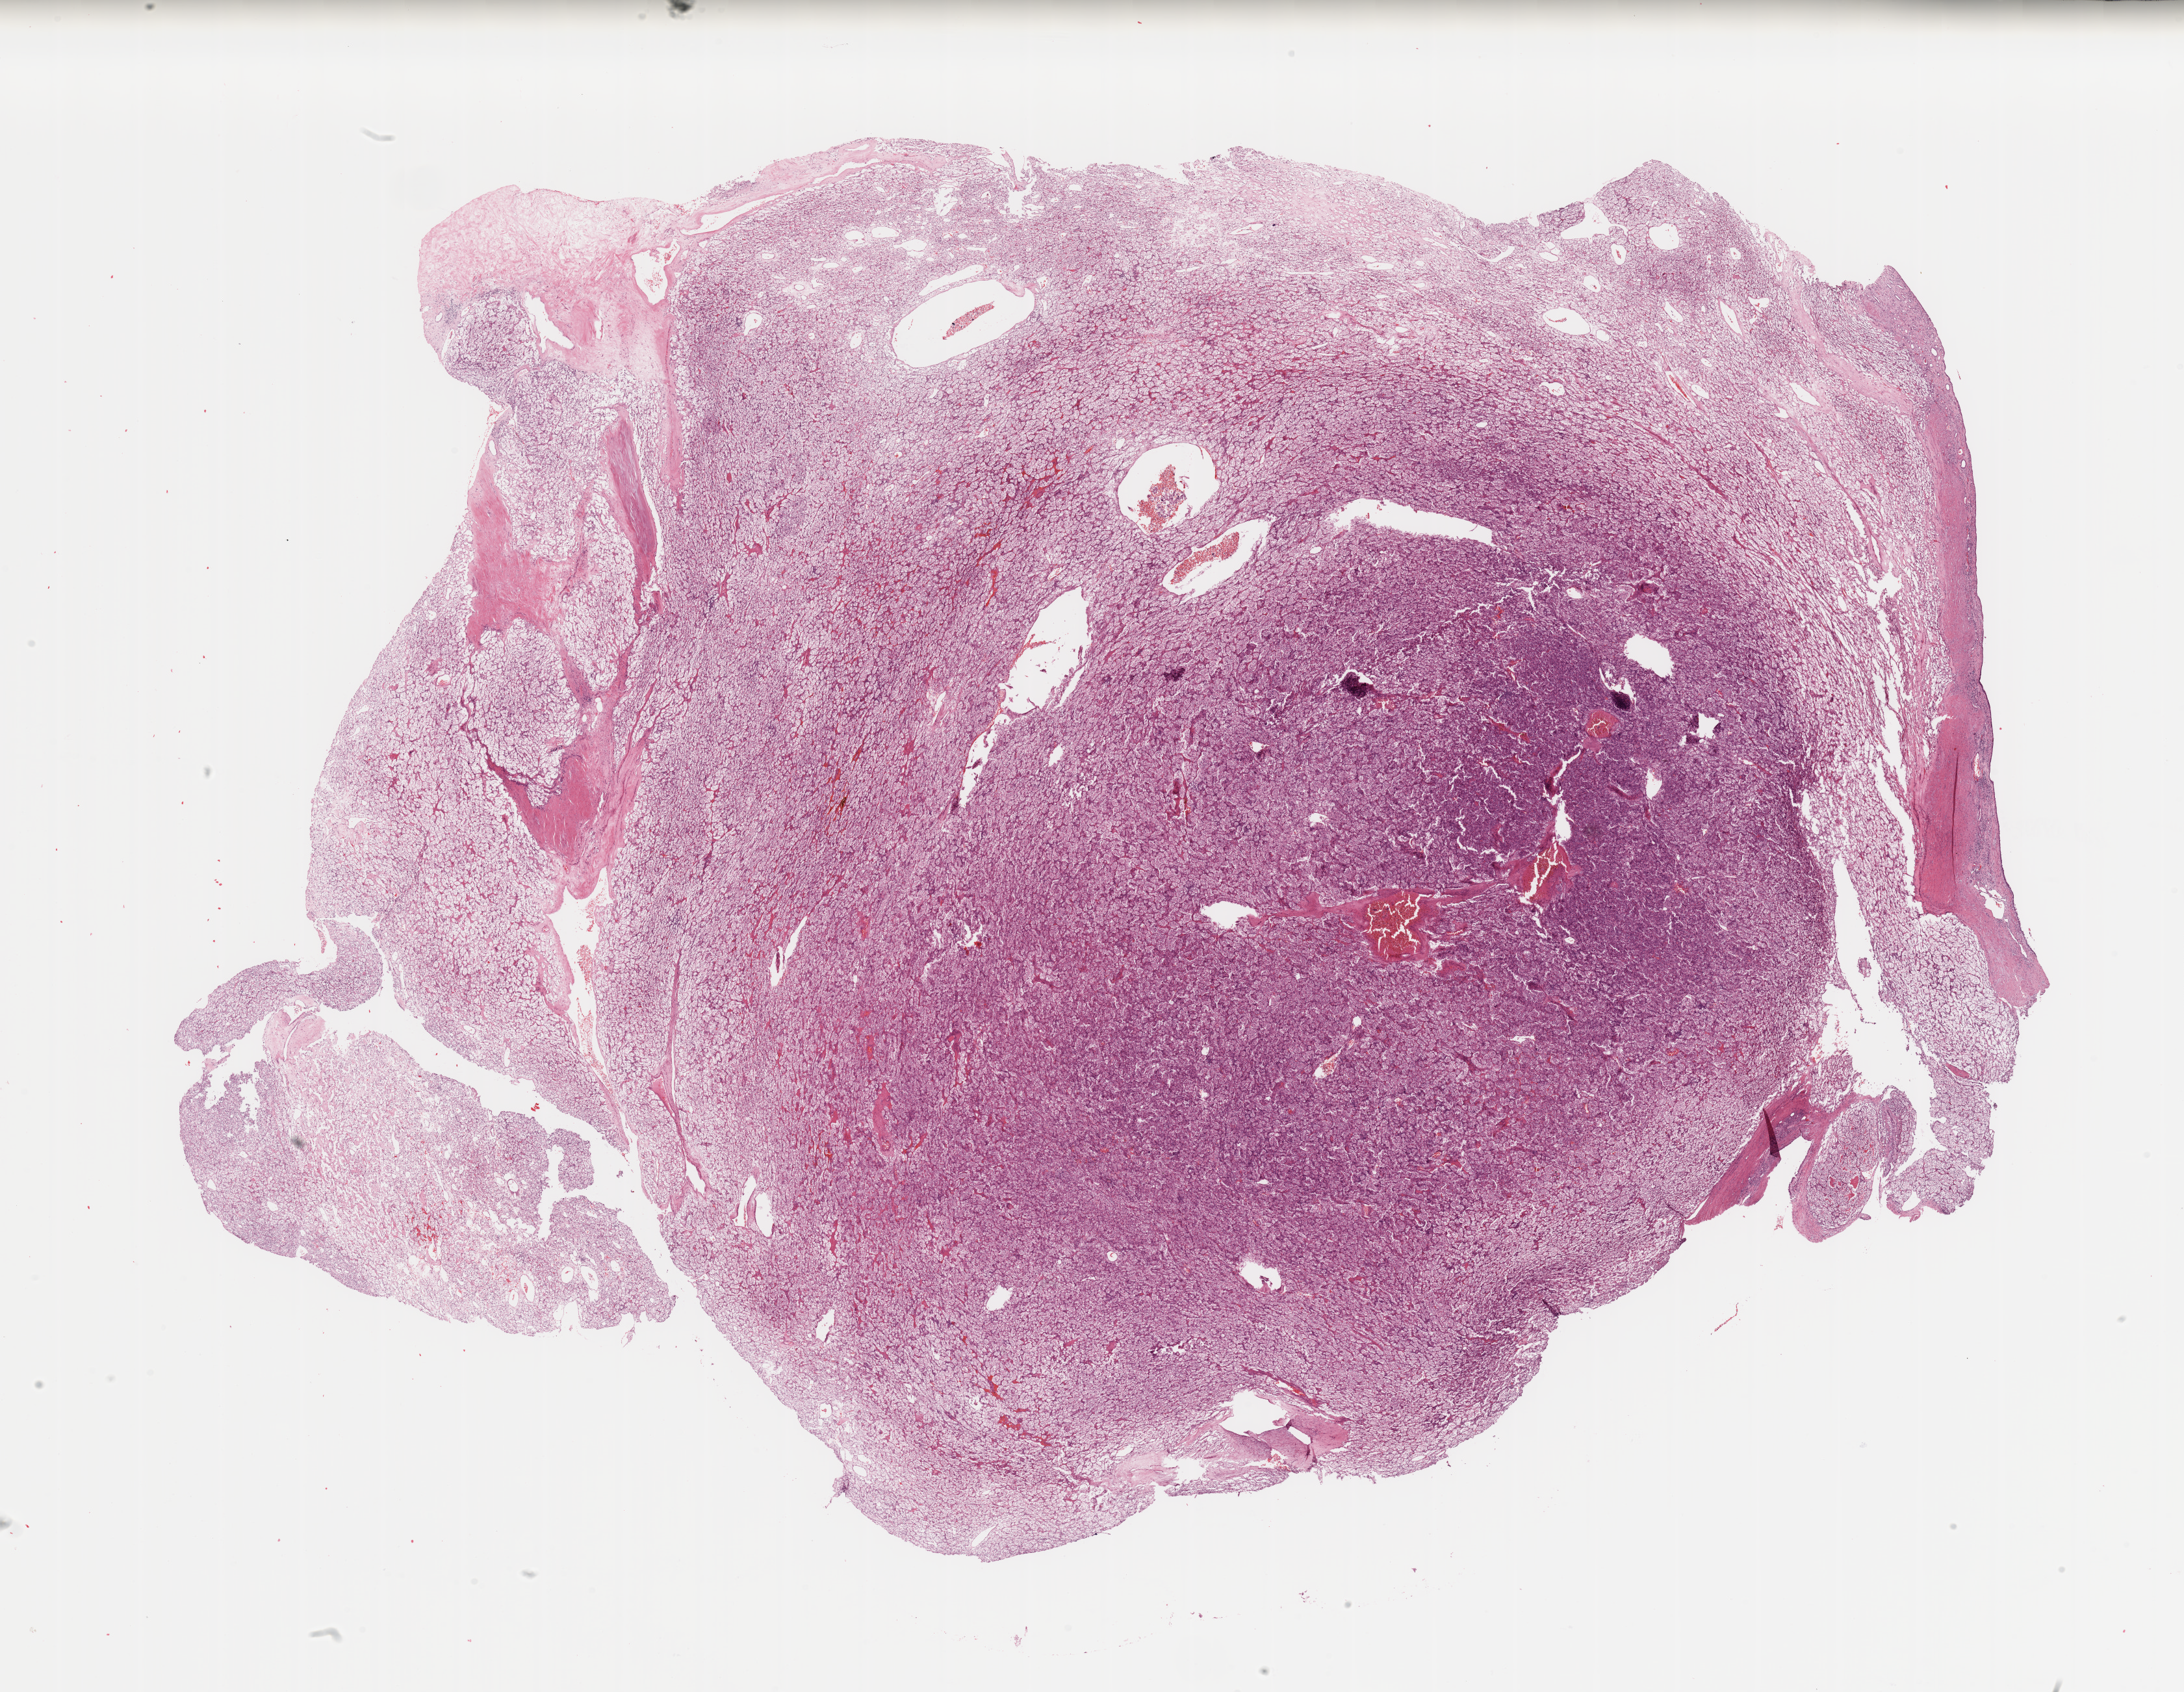
Digitized Hematoxylin and eosin (H&E) stained tissue section (whole slide), a low-resolution overview of the entire scanned area, about 26.6 x 20.6 mm. Kidney, tumour tissue. 69-year-old female patient. Histologic grade: G2 (moderately differentiated).
* histologic diagnosis: Renal cell carcinoma, NOS